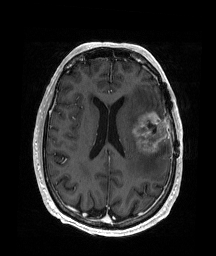
Brain MRI from a brain-tumour surgery series, one axial slice; position 78 of 176 along the scan axis; T1-weighted post-contrast; 1 mm slice thickness; 216 × 256 image matrix, field of view 219 × 260 mm. From the clinical record (not read from this slice): histopathology: Glioblastoma; WHO grade: 4; IDH mutation: no.
Annotated regions visible in this slice (expert manual segmentation):
- tumour: bounding box (x1, y1, x2, y2) in pixels: (132, 111, 169, 155)